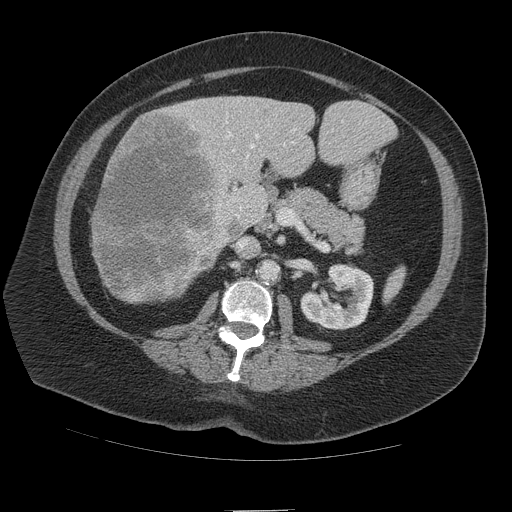
Contrast-enhanced abdominal CT (liver protocol), one axial slice. Position 47 of 109 along the scan axis. 140 kVp. Soft-tissue window (W 400 / L 40 HU). 2.5 mm slice thickness. 512 × 512 image matrix, field of view 420 × 420 mm. Case-level facts recorded for this patient, not image findings: diagnosis: hepatocellular carcinoma (patient treated with transarterial chemoembolisation; whether this scan precedes or follows treatment is not stated here); TNM stage (as recorded): Stage-IVB; Child-Pugh class: A; tumour nodularity: multinodular.
Annotated regions visible in this slice (semi-automatic segmentation, software-assisted and operator-edited):
- liver parenchyma outside the tumour (the mass and vessels are separate outlines, so this box may not span the whole liver): bounding box [x1, y1, x2, y2] px = [92, 96, 382, 292]
- mass: [90, 106, 234, 304]
- liver vessels: [226, 121, 343, 218]